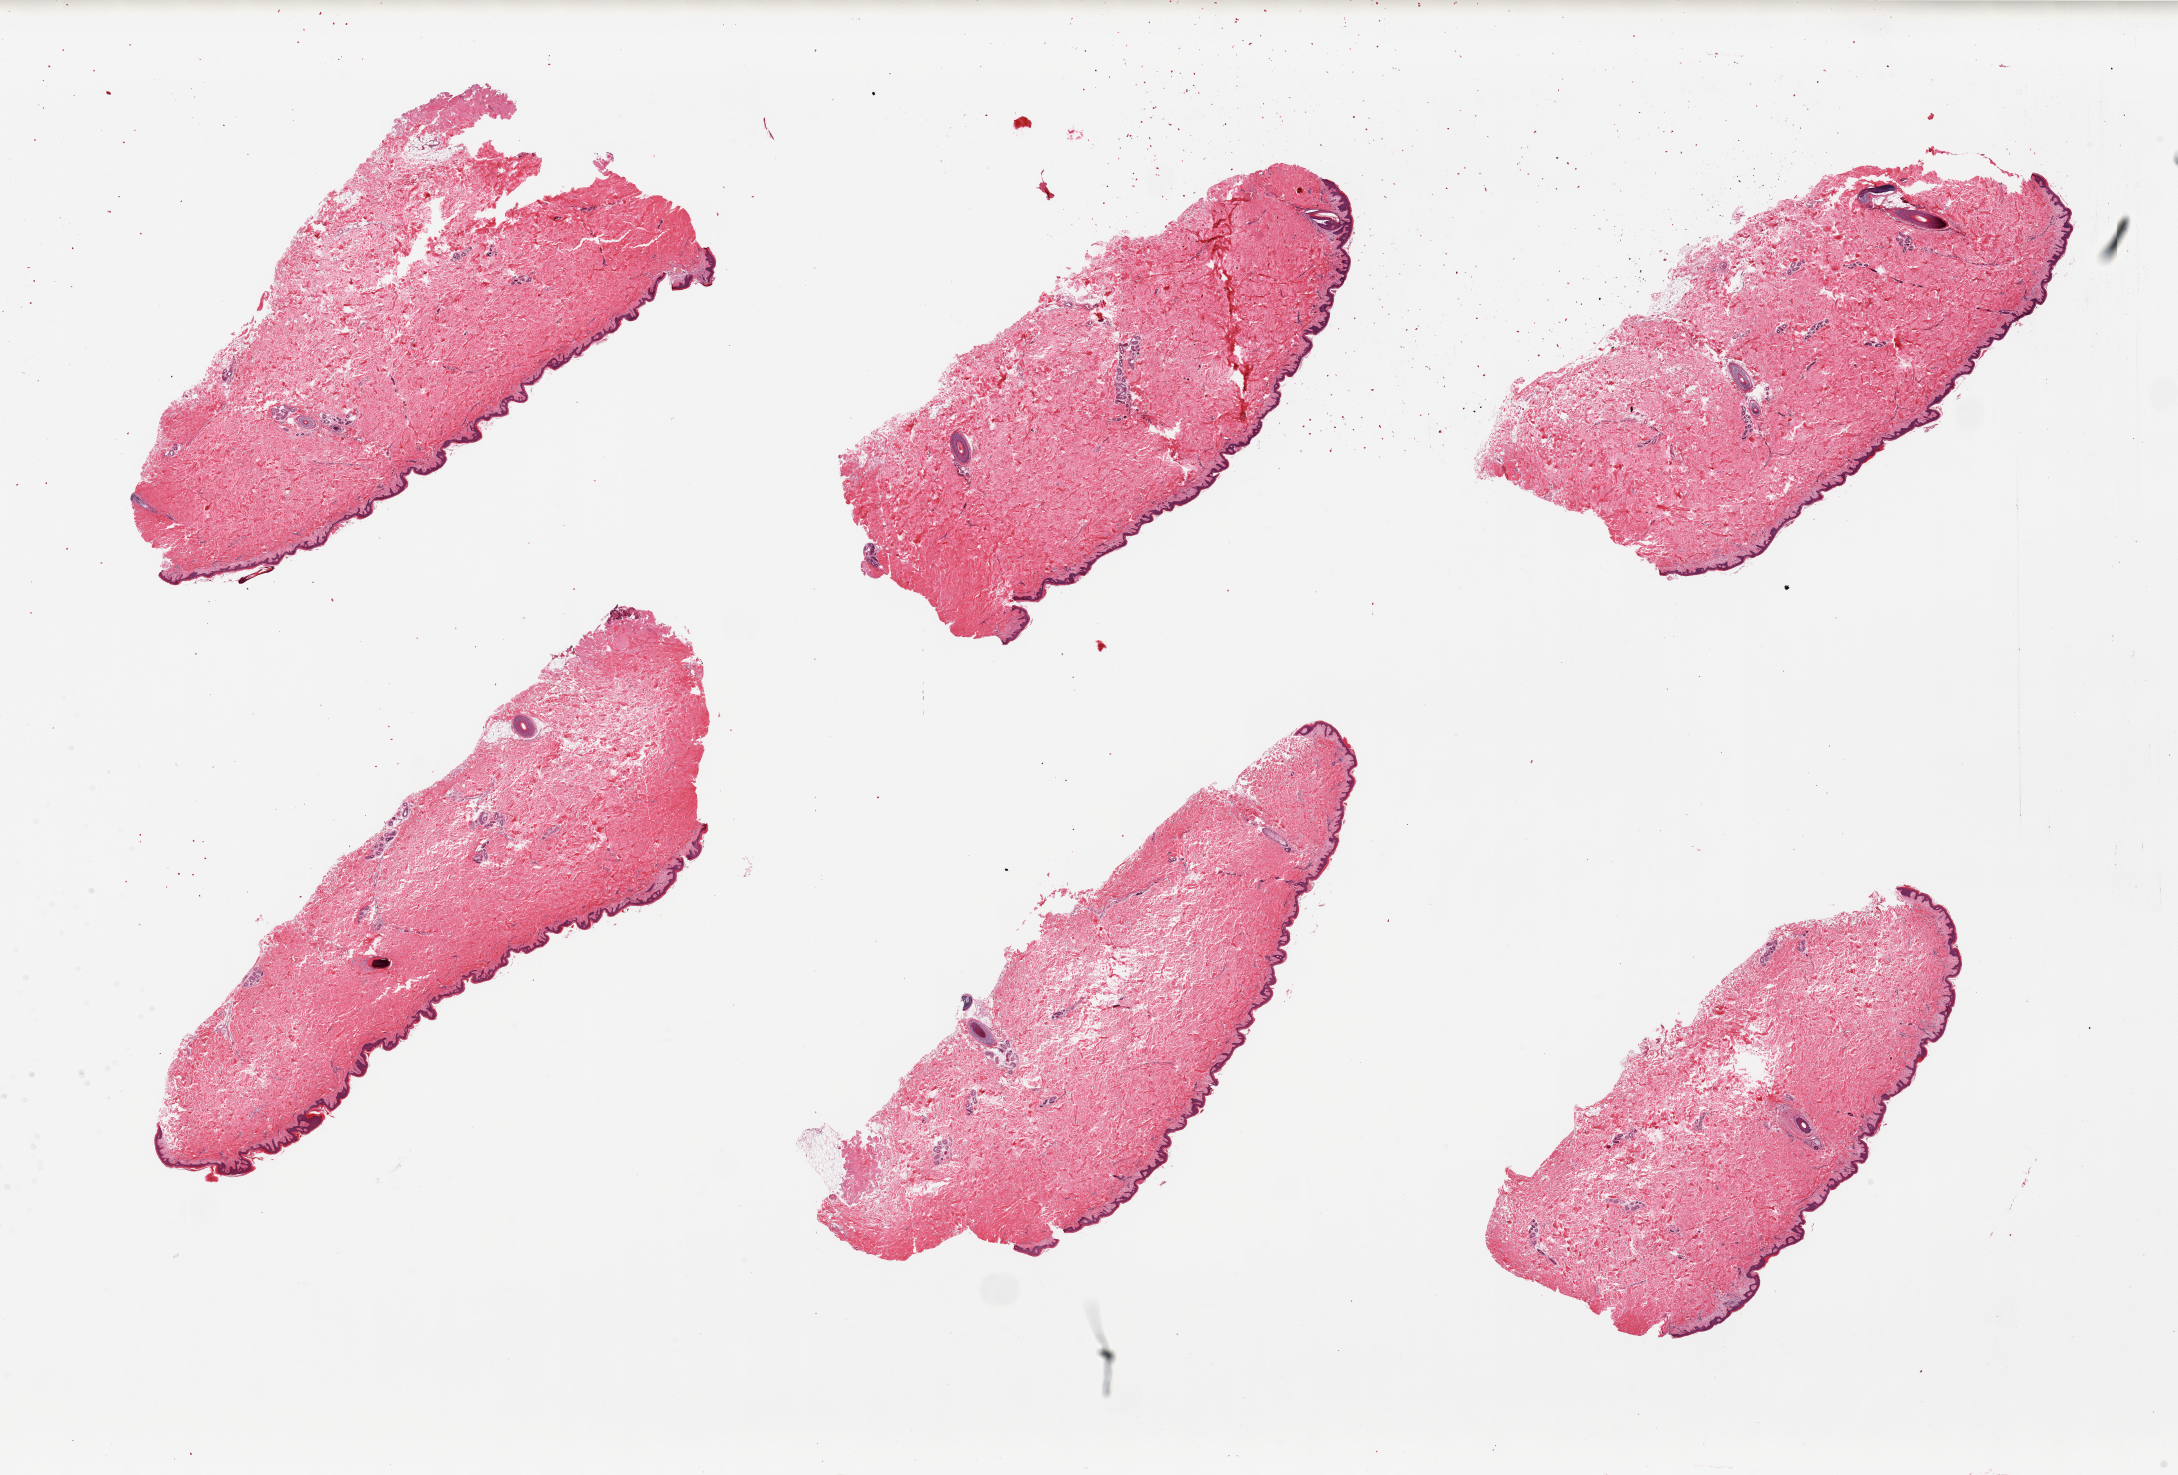
Digitized haematoxylin and eosin-stained section, brightfield, a low-resolution overview of the entire scanned area, about 34.5 x 23.3 mm (acquisition: 20x scan); PAXgene-fixed, paraffin-embedded tissue; target tissue: skin of suprapubic region; donor tissue sample. Donor: male.
• pathologist's review note for this sample: 6 pieces. Well trimmed